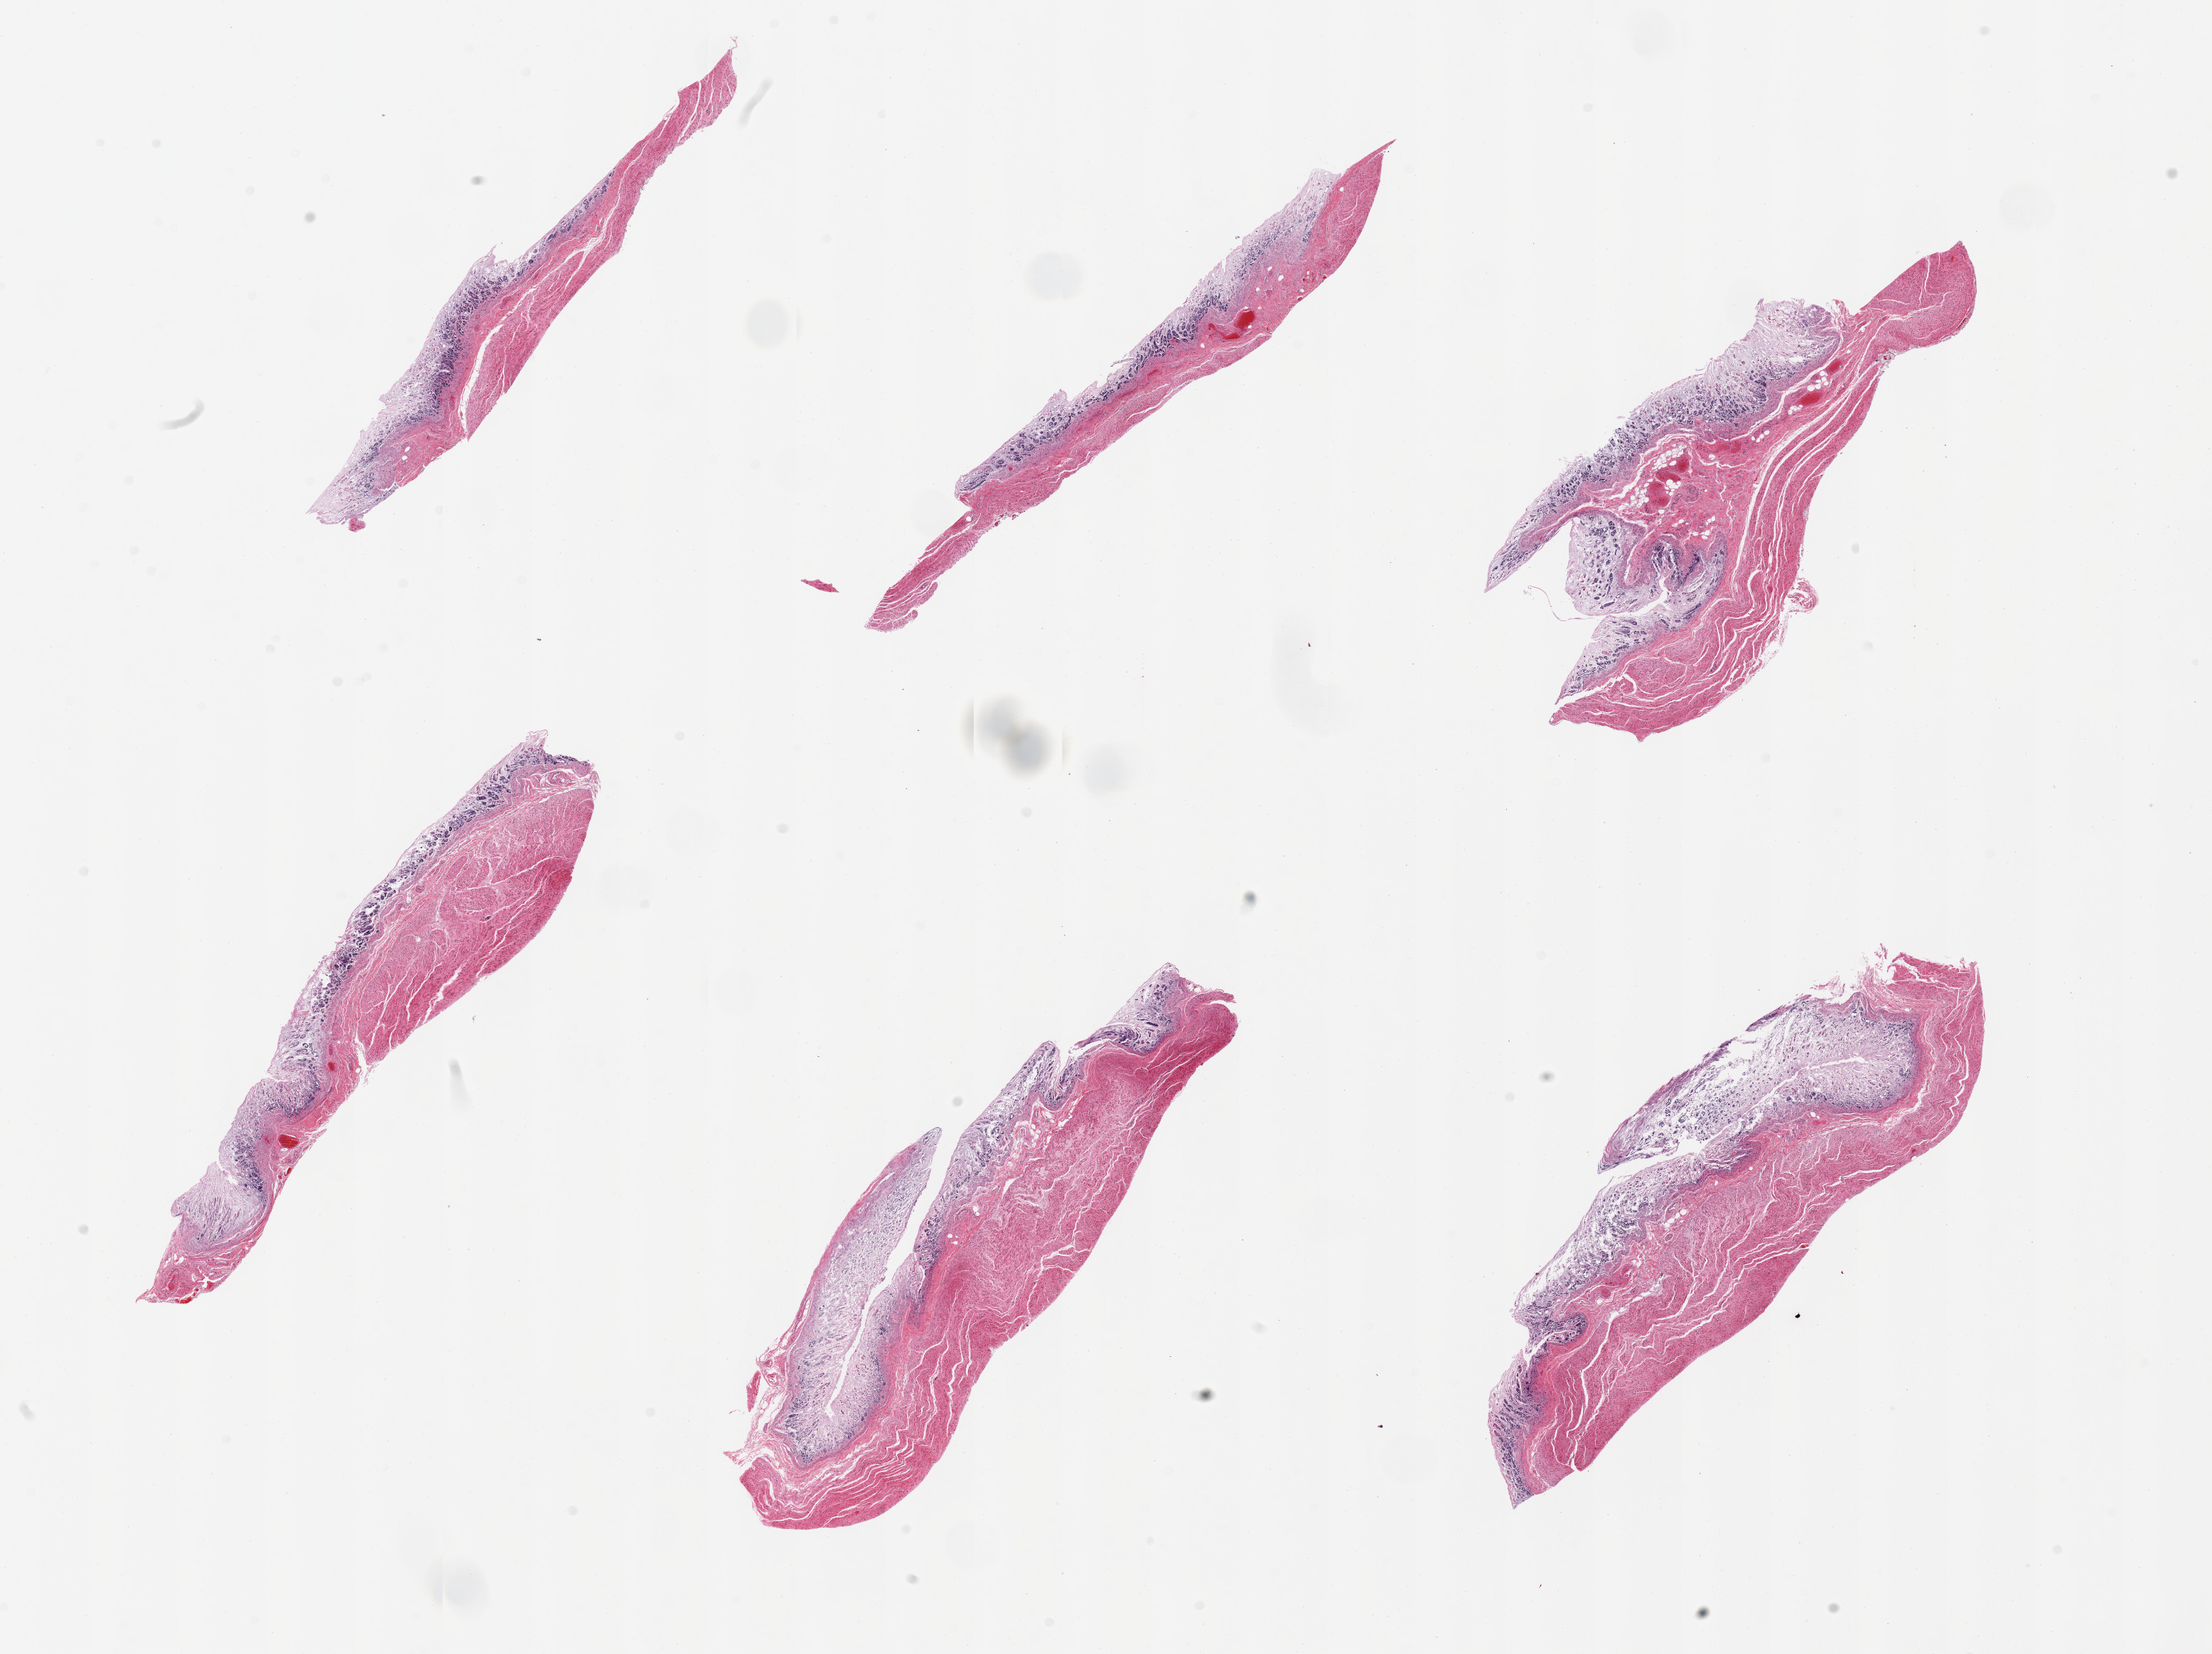
Whole-slide image, hematoxylin and eosin (H&E) stain, a low-resolution overview of the entire scanned area, about 24.6 x 18.4 mm, PAXgene-fixed paraffin-embedded (PFPE) section, section of stomach (target tissue), tissue donor sample. Female donor.
Pathologist's review note for this sample: 6 pieces, mucosa totally autolyzed.